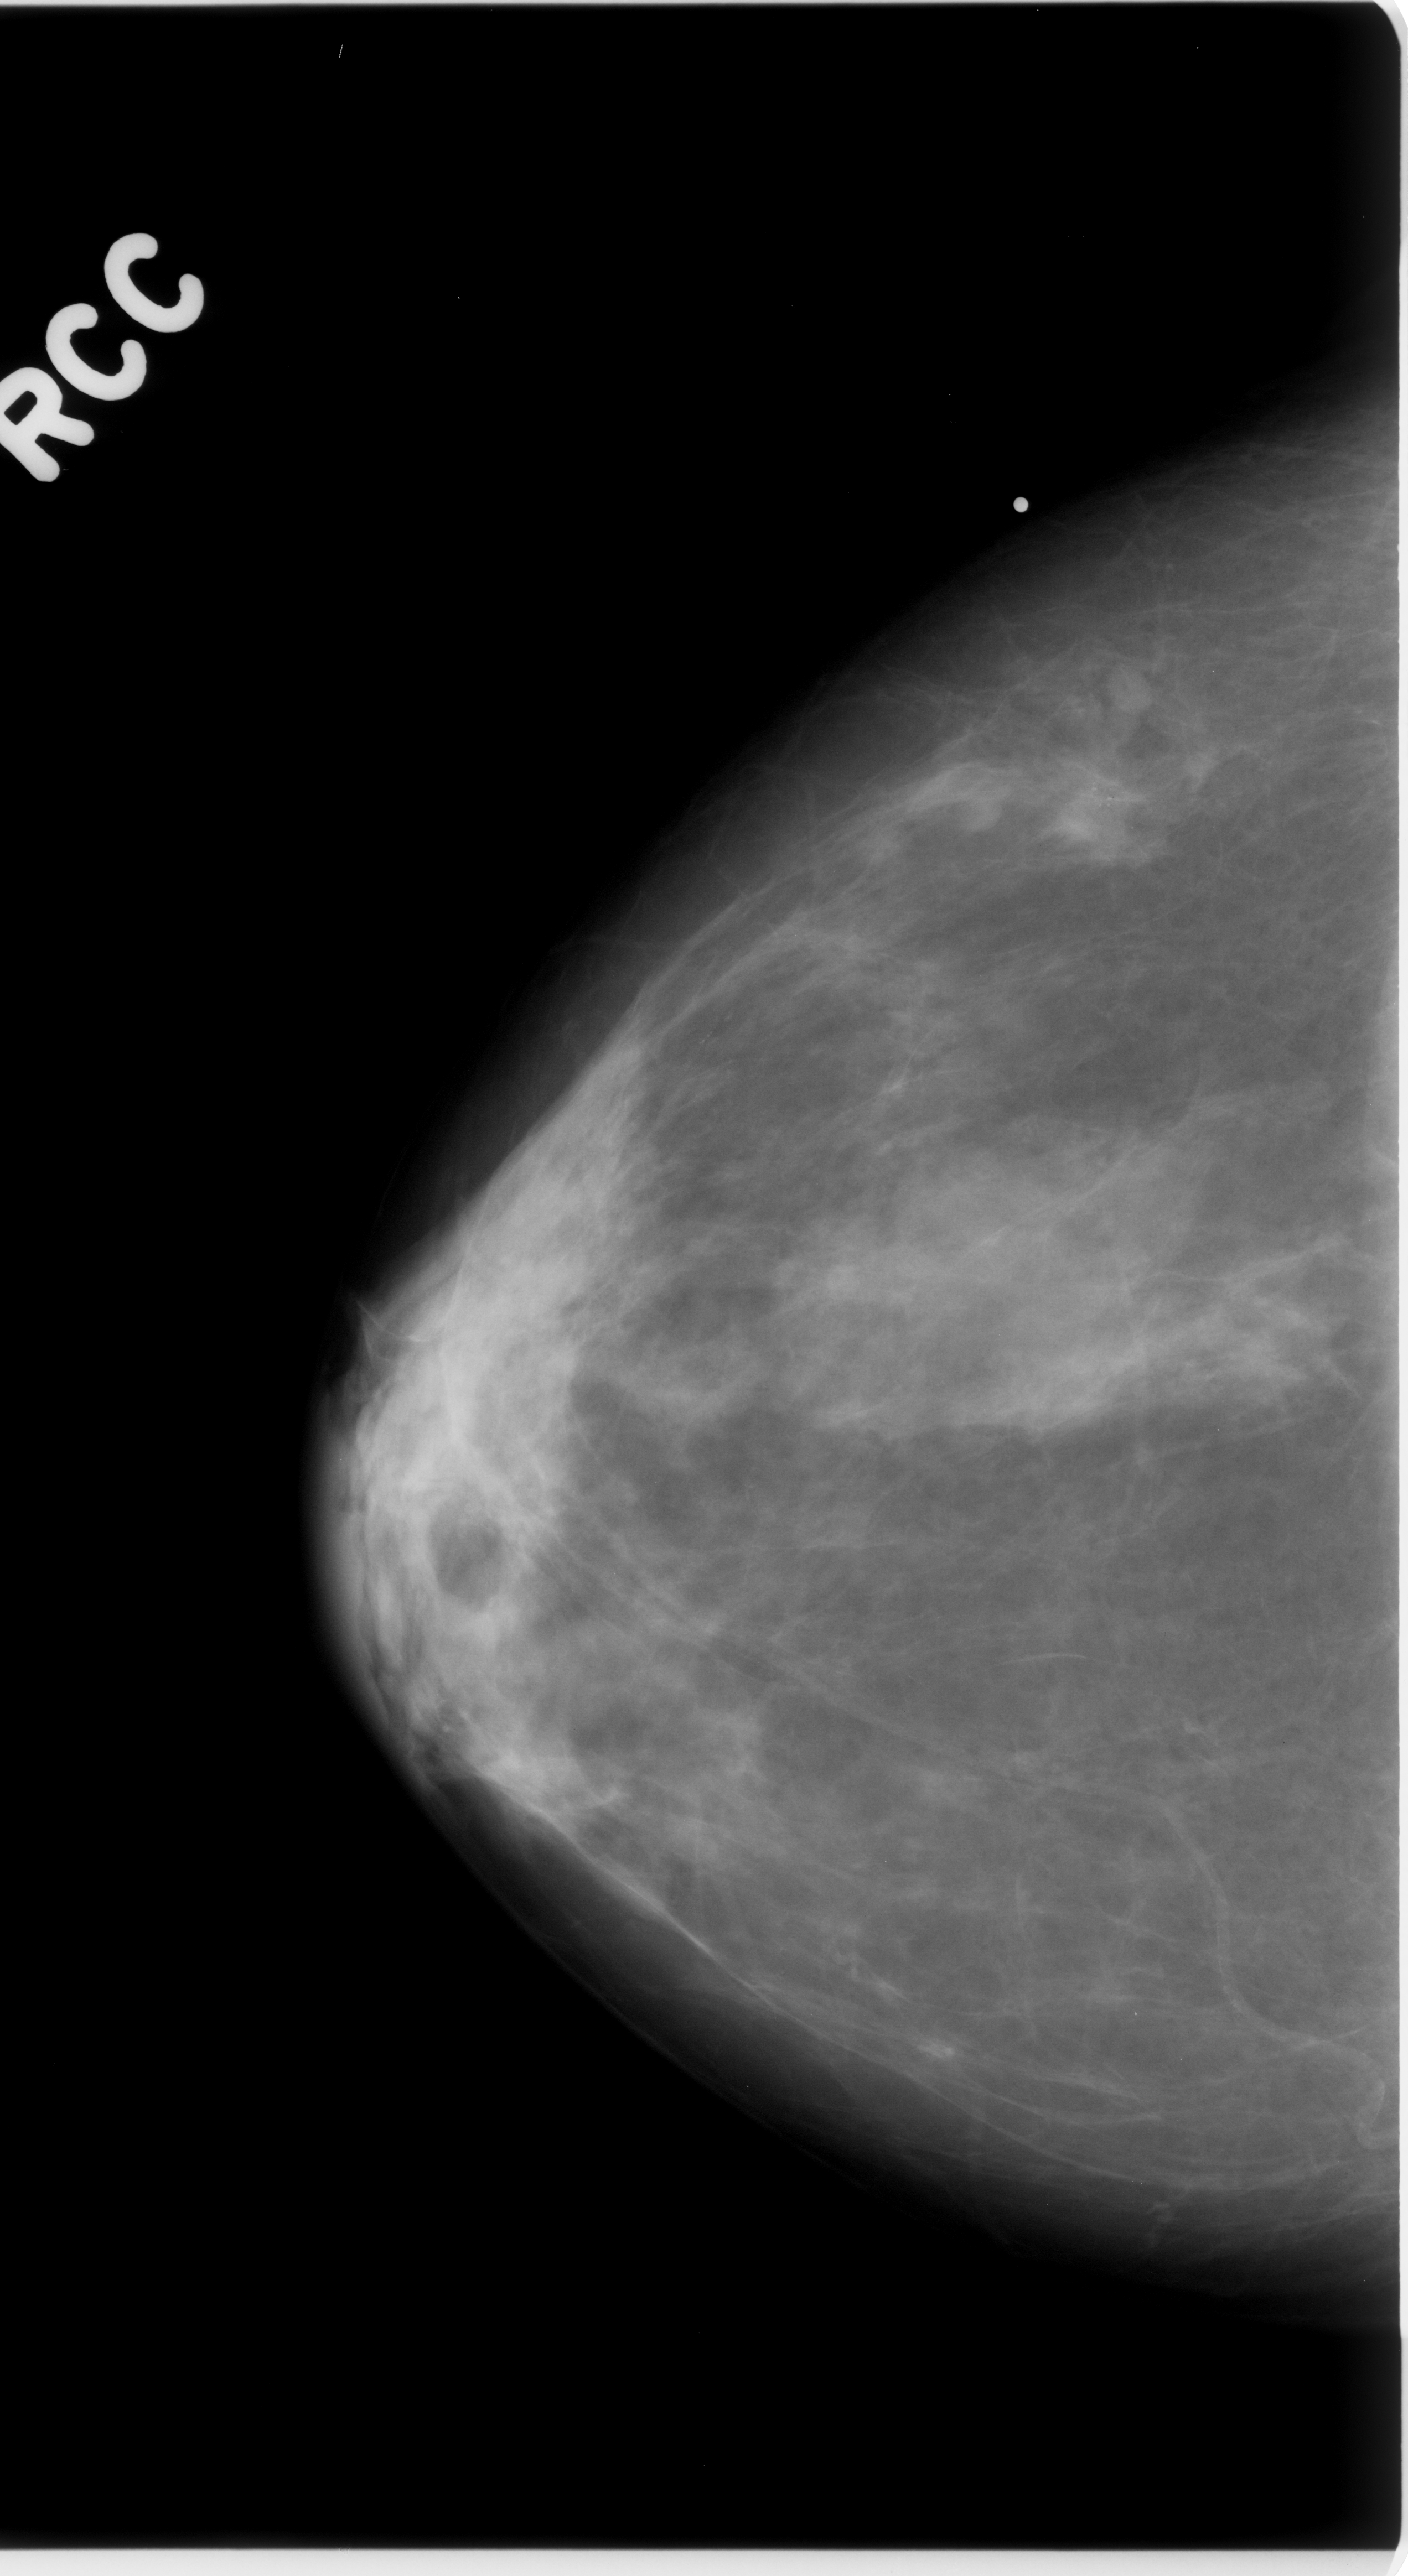
Scanned film-screen mammogram; right breast; craniocaudal (CC) view; breast composition: scattered fibroglandular densities (BI-RADS density category 2 of 4).
Marked abnormality: calcifications, morphology pleomorphic, distribution clustered; BI-RADS assessment category 5; subtlety rating 4 on a 1 (subtle) to 5 (obvious) scale; pathology result (as recorded, not read from the image): malignant.